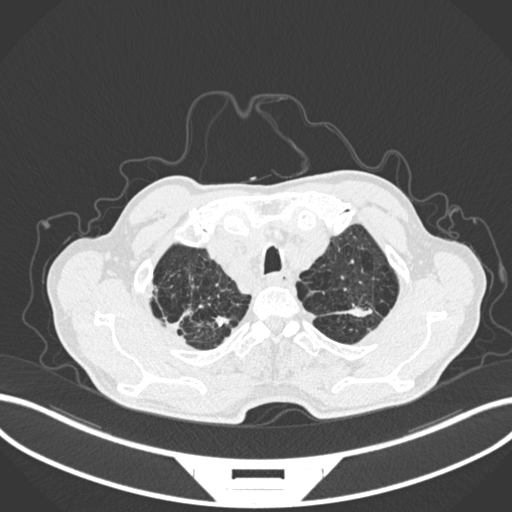
Chest CT, one axial slice. Reconstruction kernel B30f. 120 kVp. Lung window (W 1500 / L -600 HU). 1 mm slice thickness. 512 × 512 image matrix, field of view 400 × 400 mm. Male patient, age 74 years. Case-level facts recorded for this patient, not image findings: clinical TNM (as recorded): T2a N1 M0.
Structures marked on this image (rectangle marked by the reading radiologist):
- lung tumour (recorded histology: adenocarcinoma): bounding box <341,303,378,321> (left, top, right, bottom; pixels)